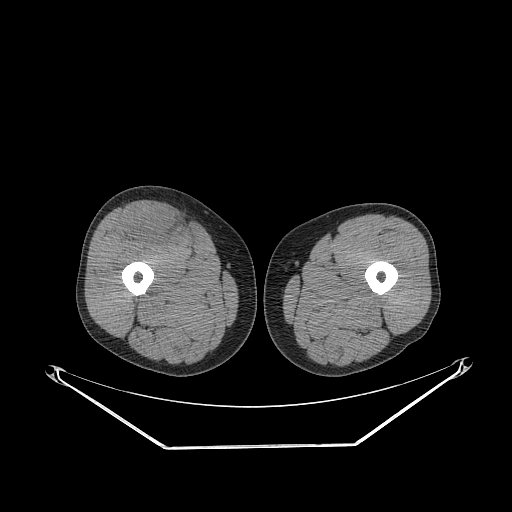
CT of an extremity soft-tissue mass (from a PET/CT study), one axial slice; slice 267 of 311 in the series (ordered by position); soft-tissue window (W 400 / L 40 HU); 3.75 mm slice thickness; 512 × 512 image matrix, field of view 500 × 500 mm. Male patient. Case-level facts recorded for this patient, not image findings: histological type: pleiomorphic leiomyosarcoma; grade: intermediate; site of the primary tumour: right thigh.
Outlined on this slice (expert contour drawn on MRI and transferred to this co-registered scan by the dataset authors):
- gross tumour volume including surrounding oedema: bounding box <126,206,181,245> (left, top, right, bottom; pixels)
- gross tumour volume (mass): <132,212,177,243>